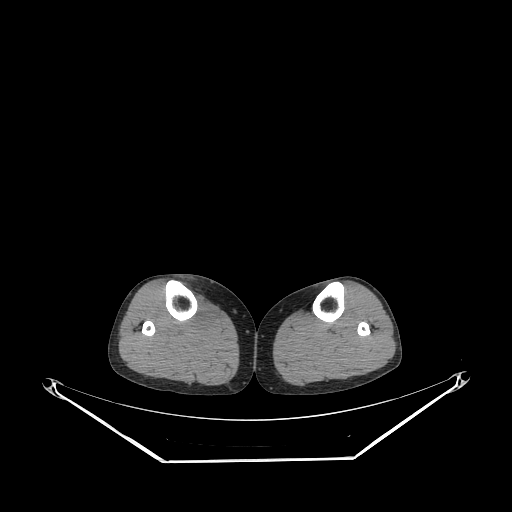
CT of an extremity soft-tissue mass (from a PET/CT study), one axial slice. Position 148 of 267 along the scan axis. Soft-tissue window (W 400 / L 40 HU). 3.75 mm slice thickness. 512 × 512 image matrix, field of view 500 × 500 mm. Female patient. Case-level facts recorded for this patient, not image findings: histological type: undifferentiated – high grade; grade: high; site of the primary tumour: right thigh.
Outlined on this slice (expert contour drawn on MRI and transferred to this co-registered scan by the dataset authors):
- gross tumour volume (mass): box from (x=187, y=297) to (x=216, y=330) px